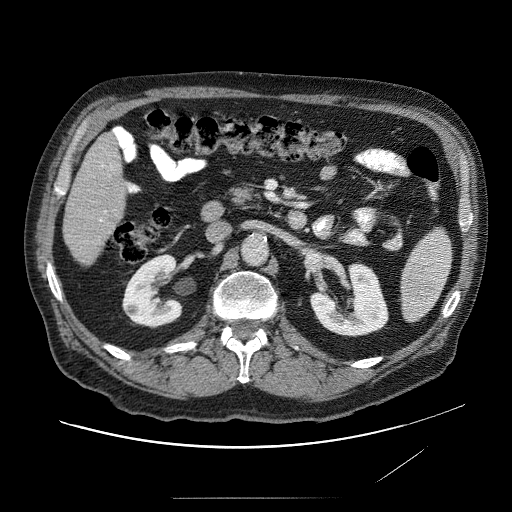
Contrast-enhanced abdominal CT (liver protocol), one axial slice. Position 18 of 89 along the scan axis. Soft-tissue window (W 400 / L 40 HU). 512 × 512 image matrix, field of view 420 × 420 mm. Case-level facts recorded for this patient, not image findings: diagnosis: hepatocellular carcinoma (patient treated with transarterial chemoembolisation; whether this scan precedes or follows treatment is not stated here); TNM stage (as recorded): Stage-IVA; Child-Pugh class: A.
Structures marked on this image (semi-automatically segmented with operator editing):
- liver parenchyma outside the tumour (the mass and vessels are separate outlines, so this box may not span the whole liver): bounding box [x1, y1, x2, y2] px = [62, 126, 132, 268]
- liver vessels: [91, 162, 121, 245]